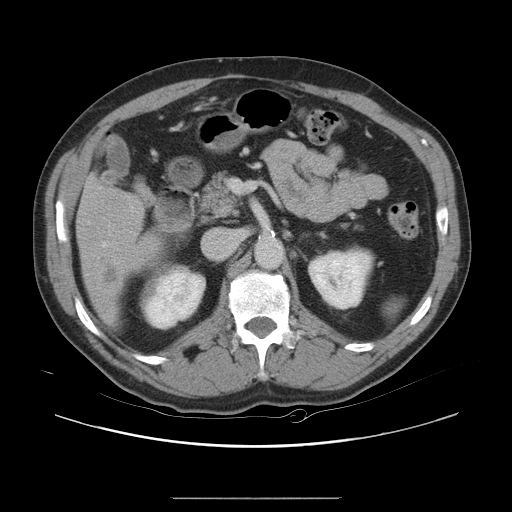
Contrast-enhanced abdominal CT, one axial slice. Slice 10 of 40 in the series (ordered by position). 120 kVp. Soft-tissue window (W 400 / L 40 HU). 512 × 512 image matrix, field of view 408 × 408 mm. Male patient, age 64 years. Case-level facts recorded for this patient, not image findings: diagnosis: colorectal cancer liver metastases, imaged before liver resection; multiple liver metastases: yes; largest metastasis: 3.2 cm; chemotherapy before resection: yes.
Structures marked on this image (manually delineated by an expert):
- hepatic veins: bounding box (x1, y1, x2, y2) in pixels: (103, 242, 106, 247)
- liver: (77, 179, 164, 322)
- liver metastasis: (99, 258, 120, 289)